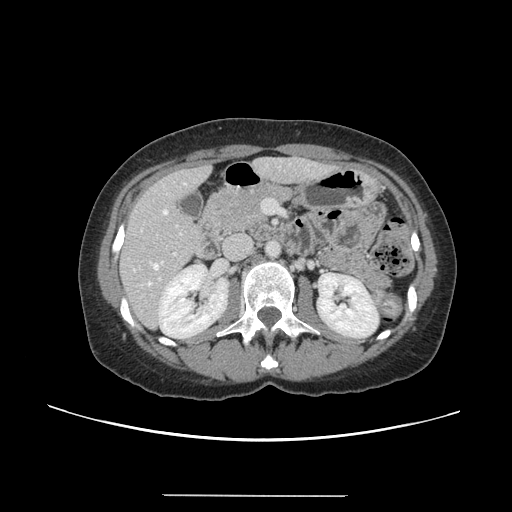
Contrast-enhanced abdominal CT, one axial slice. Slice 62 of 144 in the series (ordered by position). 120 kVp. Soft-tissue window (W 400 / L 40 HU). 2.5 mm slice thickness. 512 × 512 image matrix. Female patient, age 53 years. From the clinical record (not read from this slice): diagnosis: colorectal cancer liver metastases, imaged before liver resection; multiple liver metastases: yes; largest metastasis: 1.1 cm; disease in both lobes: no.
Outlined on this slice (manually delineated by an expert):
- hepatic veins: bounding box [x1, y1, x2, y2] px = [148, 183, 185, 285]
- liver: [122, 158, 331, 327]
- planned liver remnant (the part of the liver to remain after resection): [121, 158, 326, 308]
- portal vein (with intrahepatic branches): [158, 253, 177, 281]